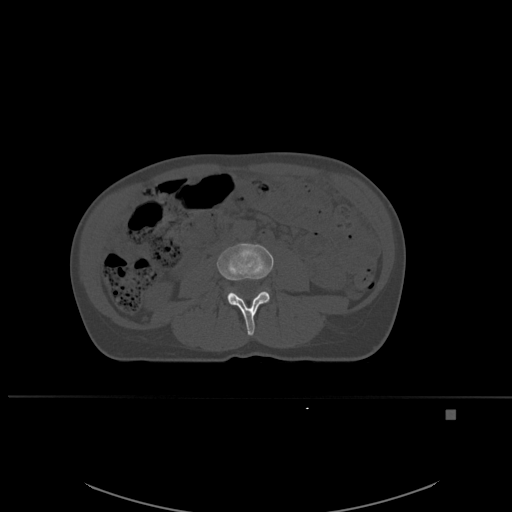
CT including the spine, one axial slice; position 207 of 537 along the scan axis; bone window (W 1800 / L 400 HU); 1.5 mm slice thickness; 512 × 512 image matrix, field of view 440 × 440 mm. Patient: female, 45 years. From the clinical record (not read from this slice): primary cancer: lung.
Annotated regions visible in this slice (semi-automatic segmentation, software-assisted and operator-edited):
- L3 vertebra: bounding box (x1, y1, x2, y2) in pixels: (217, 243, 274, 336)
- L4 vertebra: (227, 290, 233, 298)